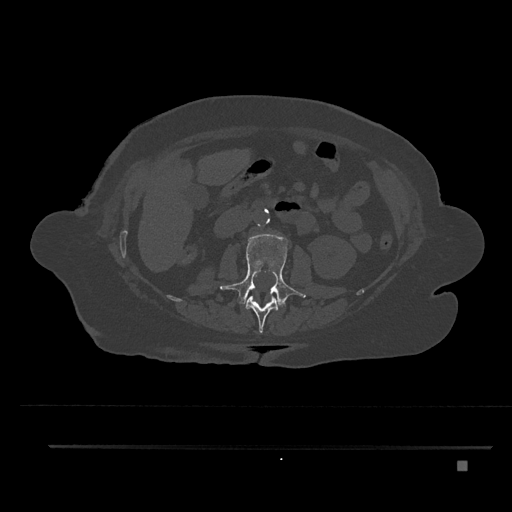
CT including the spine, one axial slice. Position 184 of 797 along the scan axis. Reconstruction kernel Br40s/3. 120 kVp. Bone window (W 1800 / L 400 HU). 0.5 mm slice thickness. 512 × 512 image matrix. Patient: female, 76 years. Case-level facts recorded for this patient, not image findings: primary cancer: lung; vertebrae with lytic lesions (as recorded): T11, L3.
Structures marked on this image (semi-automatically segmented with operator editing):
- L1 vertebra: bounding box [x1, y1, x2, y2] px = [246, 295, 279, 333]
- L2 vertebra: [220, 234, 306, 308]